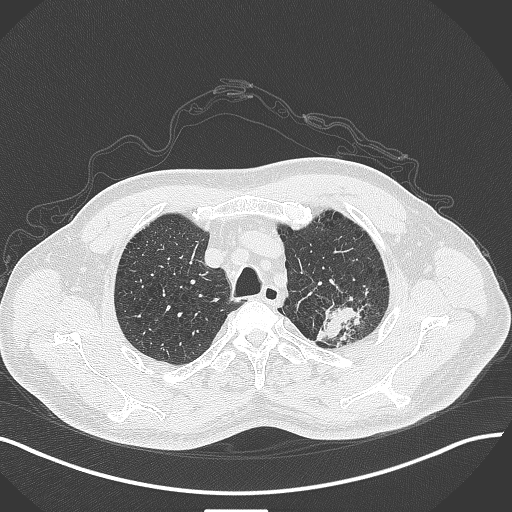
Chest CT, one axial slice. Position 350 of 429 along the scan axis. Reconstruction kernel B70f. Lung window (W 1500 / L -600 HU). 1 mm slice thickness. 512 × 512 image matrix. Patient: male, 55 years. Case-level facts recorded for this patient, not image findings: clinical TNM (as recorded): T3 N0 M1c.
Outlined on this slice (rectangle marked by the reading radiologist):
- lung tumour (recorded histology: adenocarcinoma): bounding box [x1, y1, x2, y2] px = [316, 289, 373, 346]